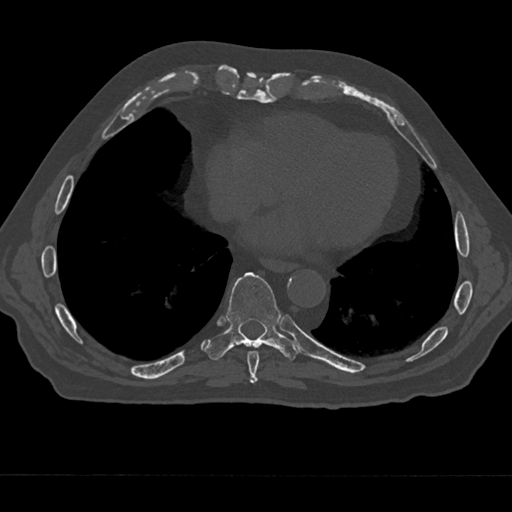
CT including the spine, one axial slice. Position 277 of 797 along the scan axis. Reconstruction kernel Br40s/3. 120 kVp. Bone window (W 1800 / L 400 HU). 0.5 mm slice thickness. 512 × 512 image matrix. Male patient, age 75 years. From the clinical record (not read from this slice): primary cancer: renal; vertebrae with lytic lesions (as recorded): T4.
Structures marked on this image (semi-automatic segmentation, software-assisted and operator-edited):
- T8 vertebra: bounding box [x1, y1, x2, y2] px = [247, 351, 260, 383]
- T9 vertebra: [205, 272, 298, 360]